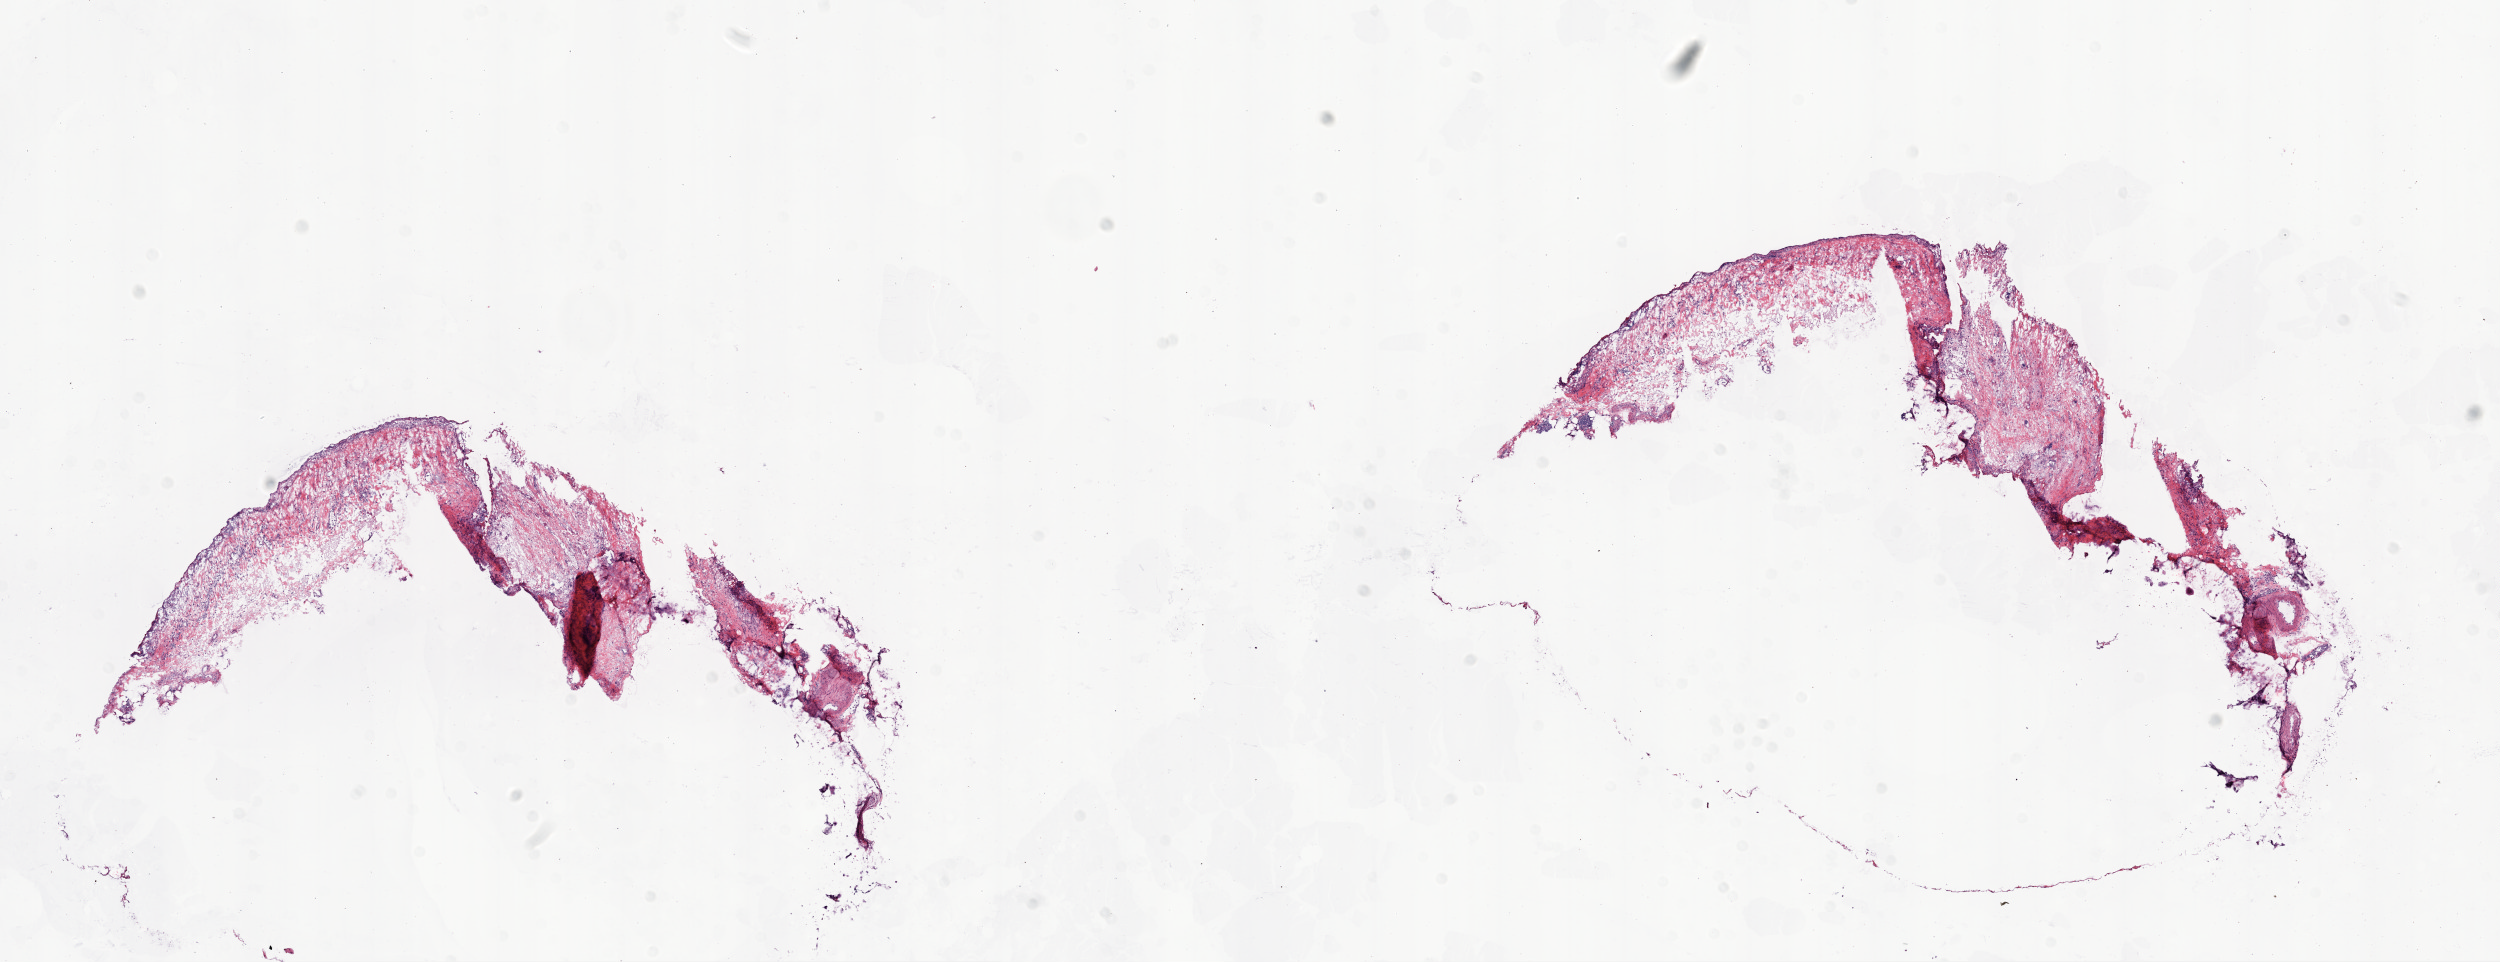
Hematoxylin and eosin (H&E) stained whole-slide image, whole scanned area (about 20.1 x 7.7 mm) shown as a low-resolution overview, frozen section from the top of the tissue portion, sample: solid tissue normal (non-tumour tissue), ovary. Female, age 50 years at initial diagnosis.
This section: solid tissue normal sample (biorepository sample class). Patient diagnosis: Serous cystadenocarcinoma, NOS.